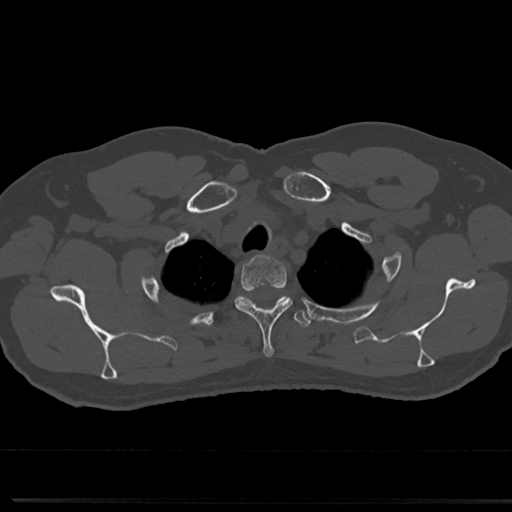
CT including the spine, one axial slice; position 624 of 817 along the scan axis; reconstruction kernel Br40s/3; bone window (W 1800 / L 400 HU); 0.5 mm slice thickness; 512 × 512 image matrix, field of view 355 × 355 mm. Patient: male, 61 years. Case-level facts recorded for this patient, not image findings: primary cancer: prostate.
Structures marked on this image (semi-automatic segmentation, software-assisted and operator-edited):
- T2 vertebra: bounding box (x1, y1, x2, y2) in pixels: (235, 258, 291, 356)
- T3 vertebra: (218, 296, 313, 358)